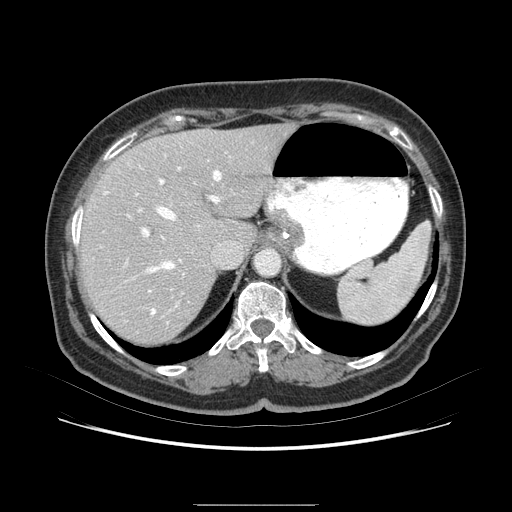
Contrast-enhanced abdominal CT (liver protocol), one axial slice. Slice 56 of 79 in the series (ordered by position). Soft-tissue window (W 400 / L 40 HU). 512 × 512 image matrix, field of view 380 × 380 mm. Case-level facts recorded for this patient, not image findings: diagnosis: hepatocellular carcinoma (patient treated with transarterial chemoembolisation; whether this scan precedes or follows treatment is not stated here); TNM stage (as recorded): Stage-I; Child-Pugh class: A; tumour differentiation: poorly differentiated; tumour nodularity: uninodular.
Outlined on this slice (semi-automatic segmentation, software-assisted and operator-edited):
- abdominal aorta: bounding box (x1, y1, x2, y2) in pixels: (257, 251, 282, 277)
- liver parenchyma outside the tumour (the mass and vessels are separate outlines, so this box may not span the whole liver): (80, 128, 300, 332)
- liver vessels: (135, 159, 240, 246)